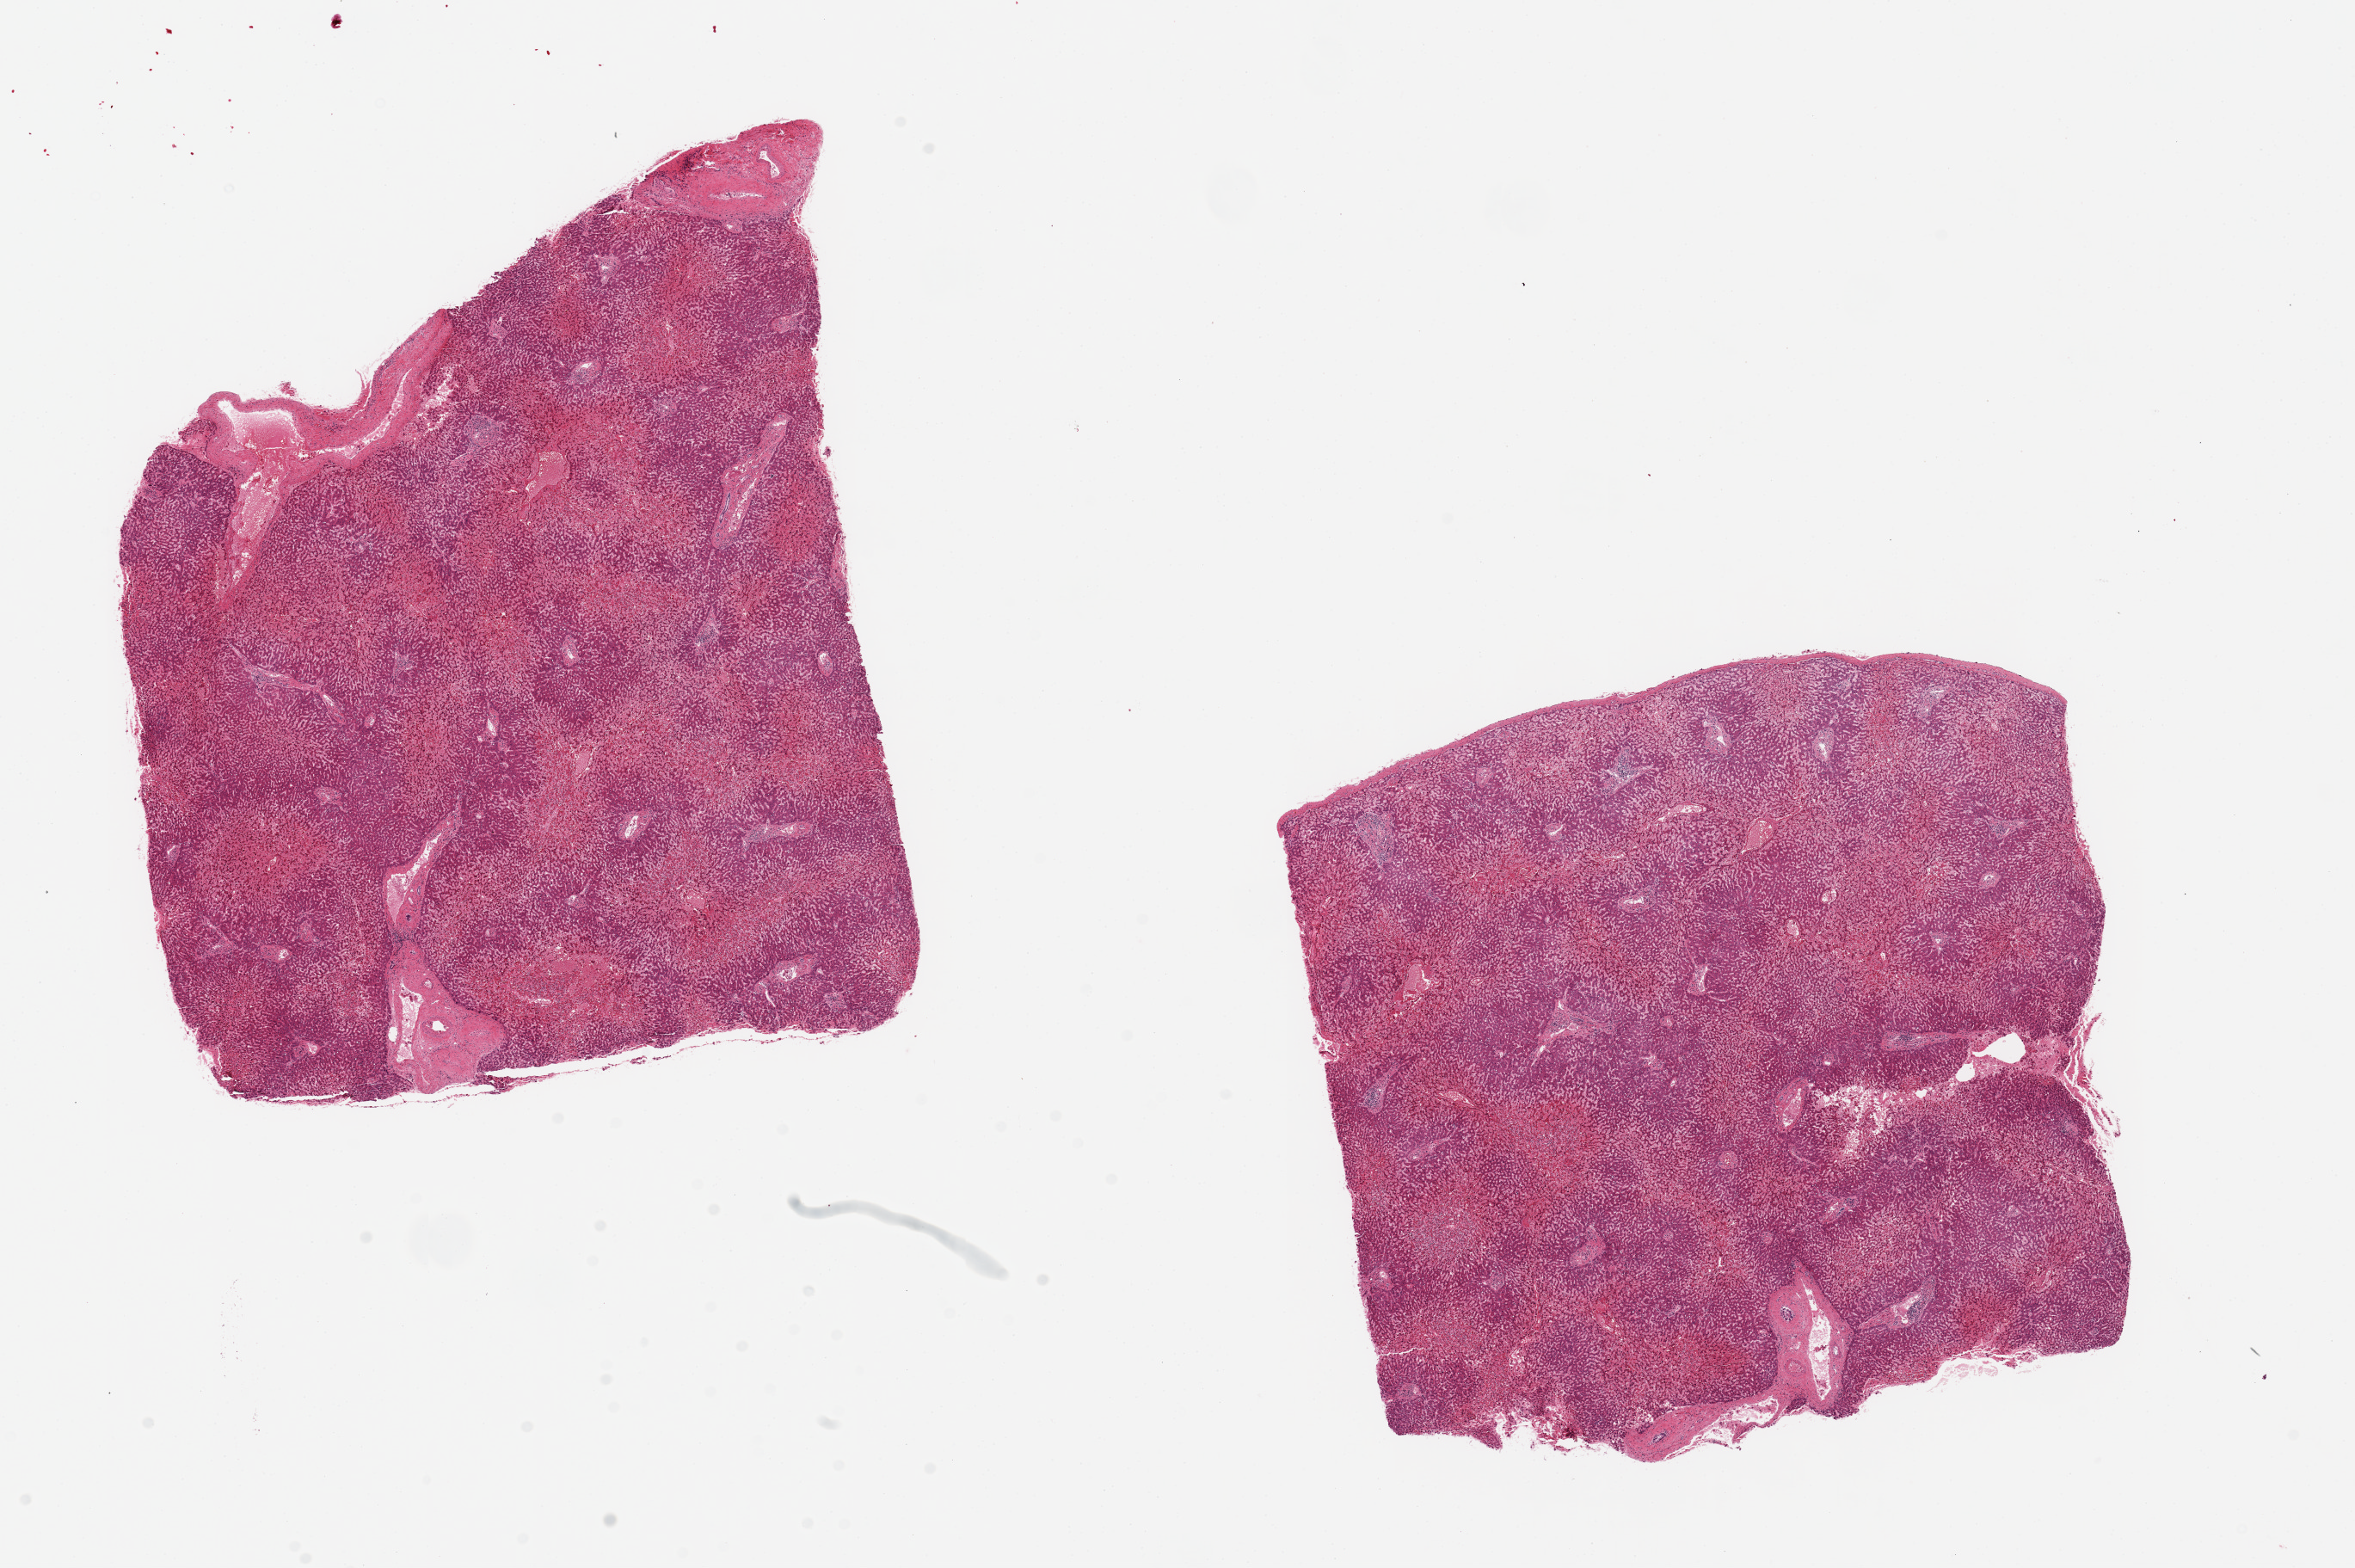
Whole-slide image, hematoxylin and eosin (H&E) stain, brightfield, whole scanned area (about 21.7 x 14.4 mm) shown as a low-resolution overview, PAXgene-fixed, paraffin-embedded tissue, sampled site (target tissue): liver, tissue donor sample. Donor sex: female.
Review note (as recorded): 2 pieces, 8x7 & 7.5x7mm; moderate central congestion and atrophy; no fibrosis or fat.